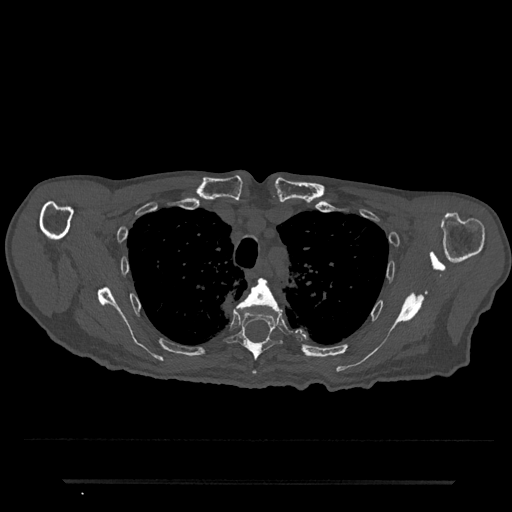
CT including the spine, one axial slice. 120 kVp. Bone window (W 1800 / L 400 HU). 0.5 mm slice thickness. 512 × 512 image matrix. Male patient, age 74 years. From the clinical record (not read from this slice): primary cancer: prostate.
Structures marked on this image (semi-automatically segmented with operator editing):
- T4 vertebra: box from (x=240, y=278) to (x=283, y=374) px
- T5 vertebra: (x=224, y=303)–(x=283, y=361)